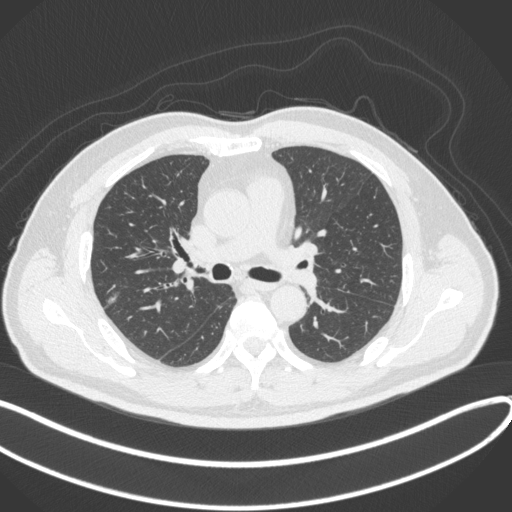
Chest CT, one axial slice. Position 207 of 373 along the scan axis. Reconstruction kernel B31f. 120 kVp. Lung window (W 1500 / L -600 HU). 1 mm slice thickness. 512 × 512 image matrix, field of view 400 × 400 mm. Patient: male, 60 years. From the clinical record (not read from this slice): clinical TNM (as recorded): T1c N0 M0.
Outlined on this slice (bounding box drawn by a radiologist):
- lung tumour (recorded histology: adenocarcinoma): bounding box [x1, y1, x2, y2] px = [101, 283, 125, 307]